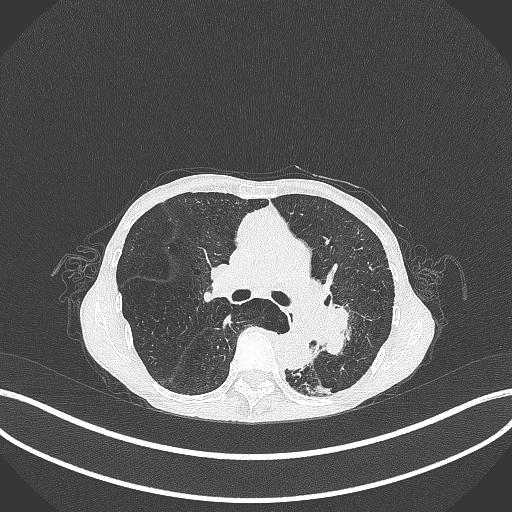
Chest CT, one axial slice; position 169 of 347 along the scan axis; reconstruction kernel B70f; 120 kVp; lung window (W 1500 / L -600 HU); 1 mm slice thickness; 512 × 512 image matrix, field of view 400 × 400 mm. Patient: female, 70 years. Case-level facts recorded for this patient, not image findings: clinical TNM (as recorded): T3 N0 M0.
Annotated regions visible in this slice (bounding box drawn by a radiologist):
- lung tumour (recorded histology: small cell carcinoma): bounding box <316,293,365,368> (left, top, right, bottom; pixels)